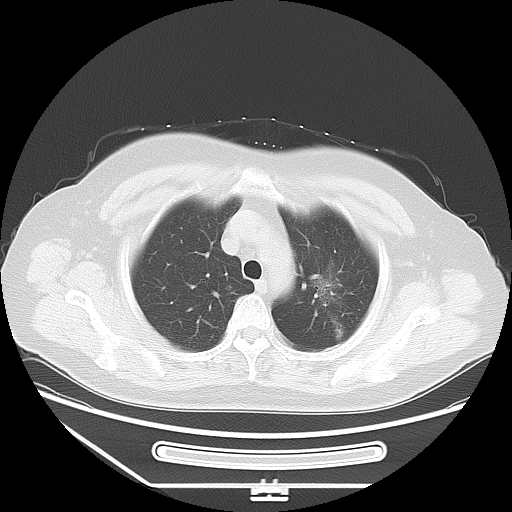
Chest CT, one axial slice. Slice 44 of 53 in the series (ordered by position). Reconstruction kernel LUNG. Lung window (W 1500 / L -600 HU). 512 × 512 image matrix. Patient: female, 66 years. Case-level facts recorded for this patient, not image findings: clinical TNM (as recorded): T2 N0 M0.
Outlined on this slice (bounding box drawn by a radiologist):
- lung tumour (recorded histology: adenocarcinoma): box from (x=307, y=252) to (x=355, y=323) px